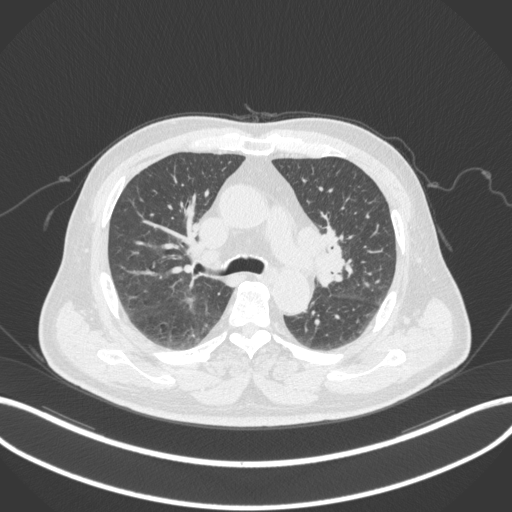
Chest CT, one axial slice; reconstruction kernel B31f; lung window (W 1500 / L -600 HU); 1 mm slice thickness; 512 × 512 image matrix, field of view 400 × 400 mm. Patient: male, 67 years. From the clinical record (not read from this slice): clinical TNM (as recorded): T2a N1 M0; histopathological grade: G3.
Structures marked on this image (rectangle marked by the reading radiologist):
- lung tumour (recorded histology: adenocarcinoma): box from (x=309, y=238) to (x=347, y=289) px